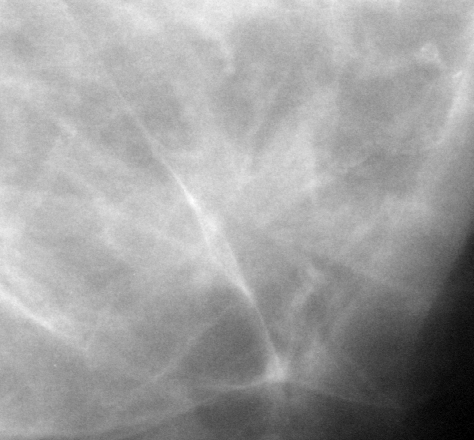
Region of interest cut from a scanned film mammogram (one marked finding); left breast; MLO view.
- Finding: mass, shape irregular, margins ill defined; BI-RADS assessment category 5; subtlety rating 4 on a 1 (subtle) to 5 (obvious) scale; pathology (as recorded): malignant.